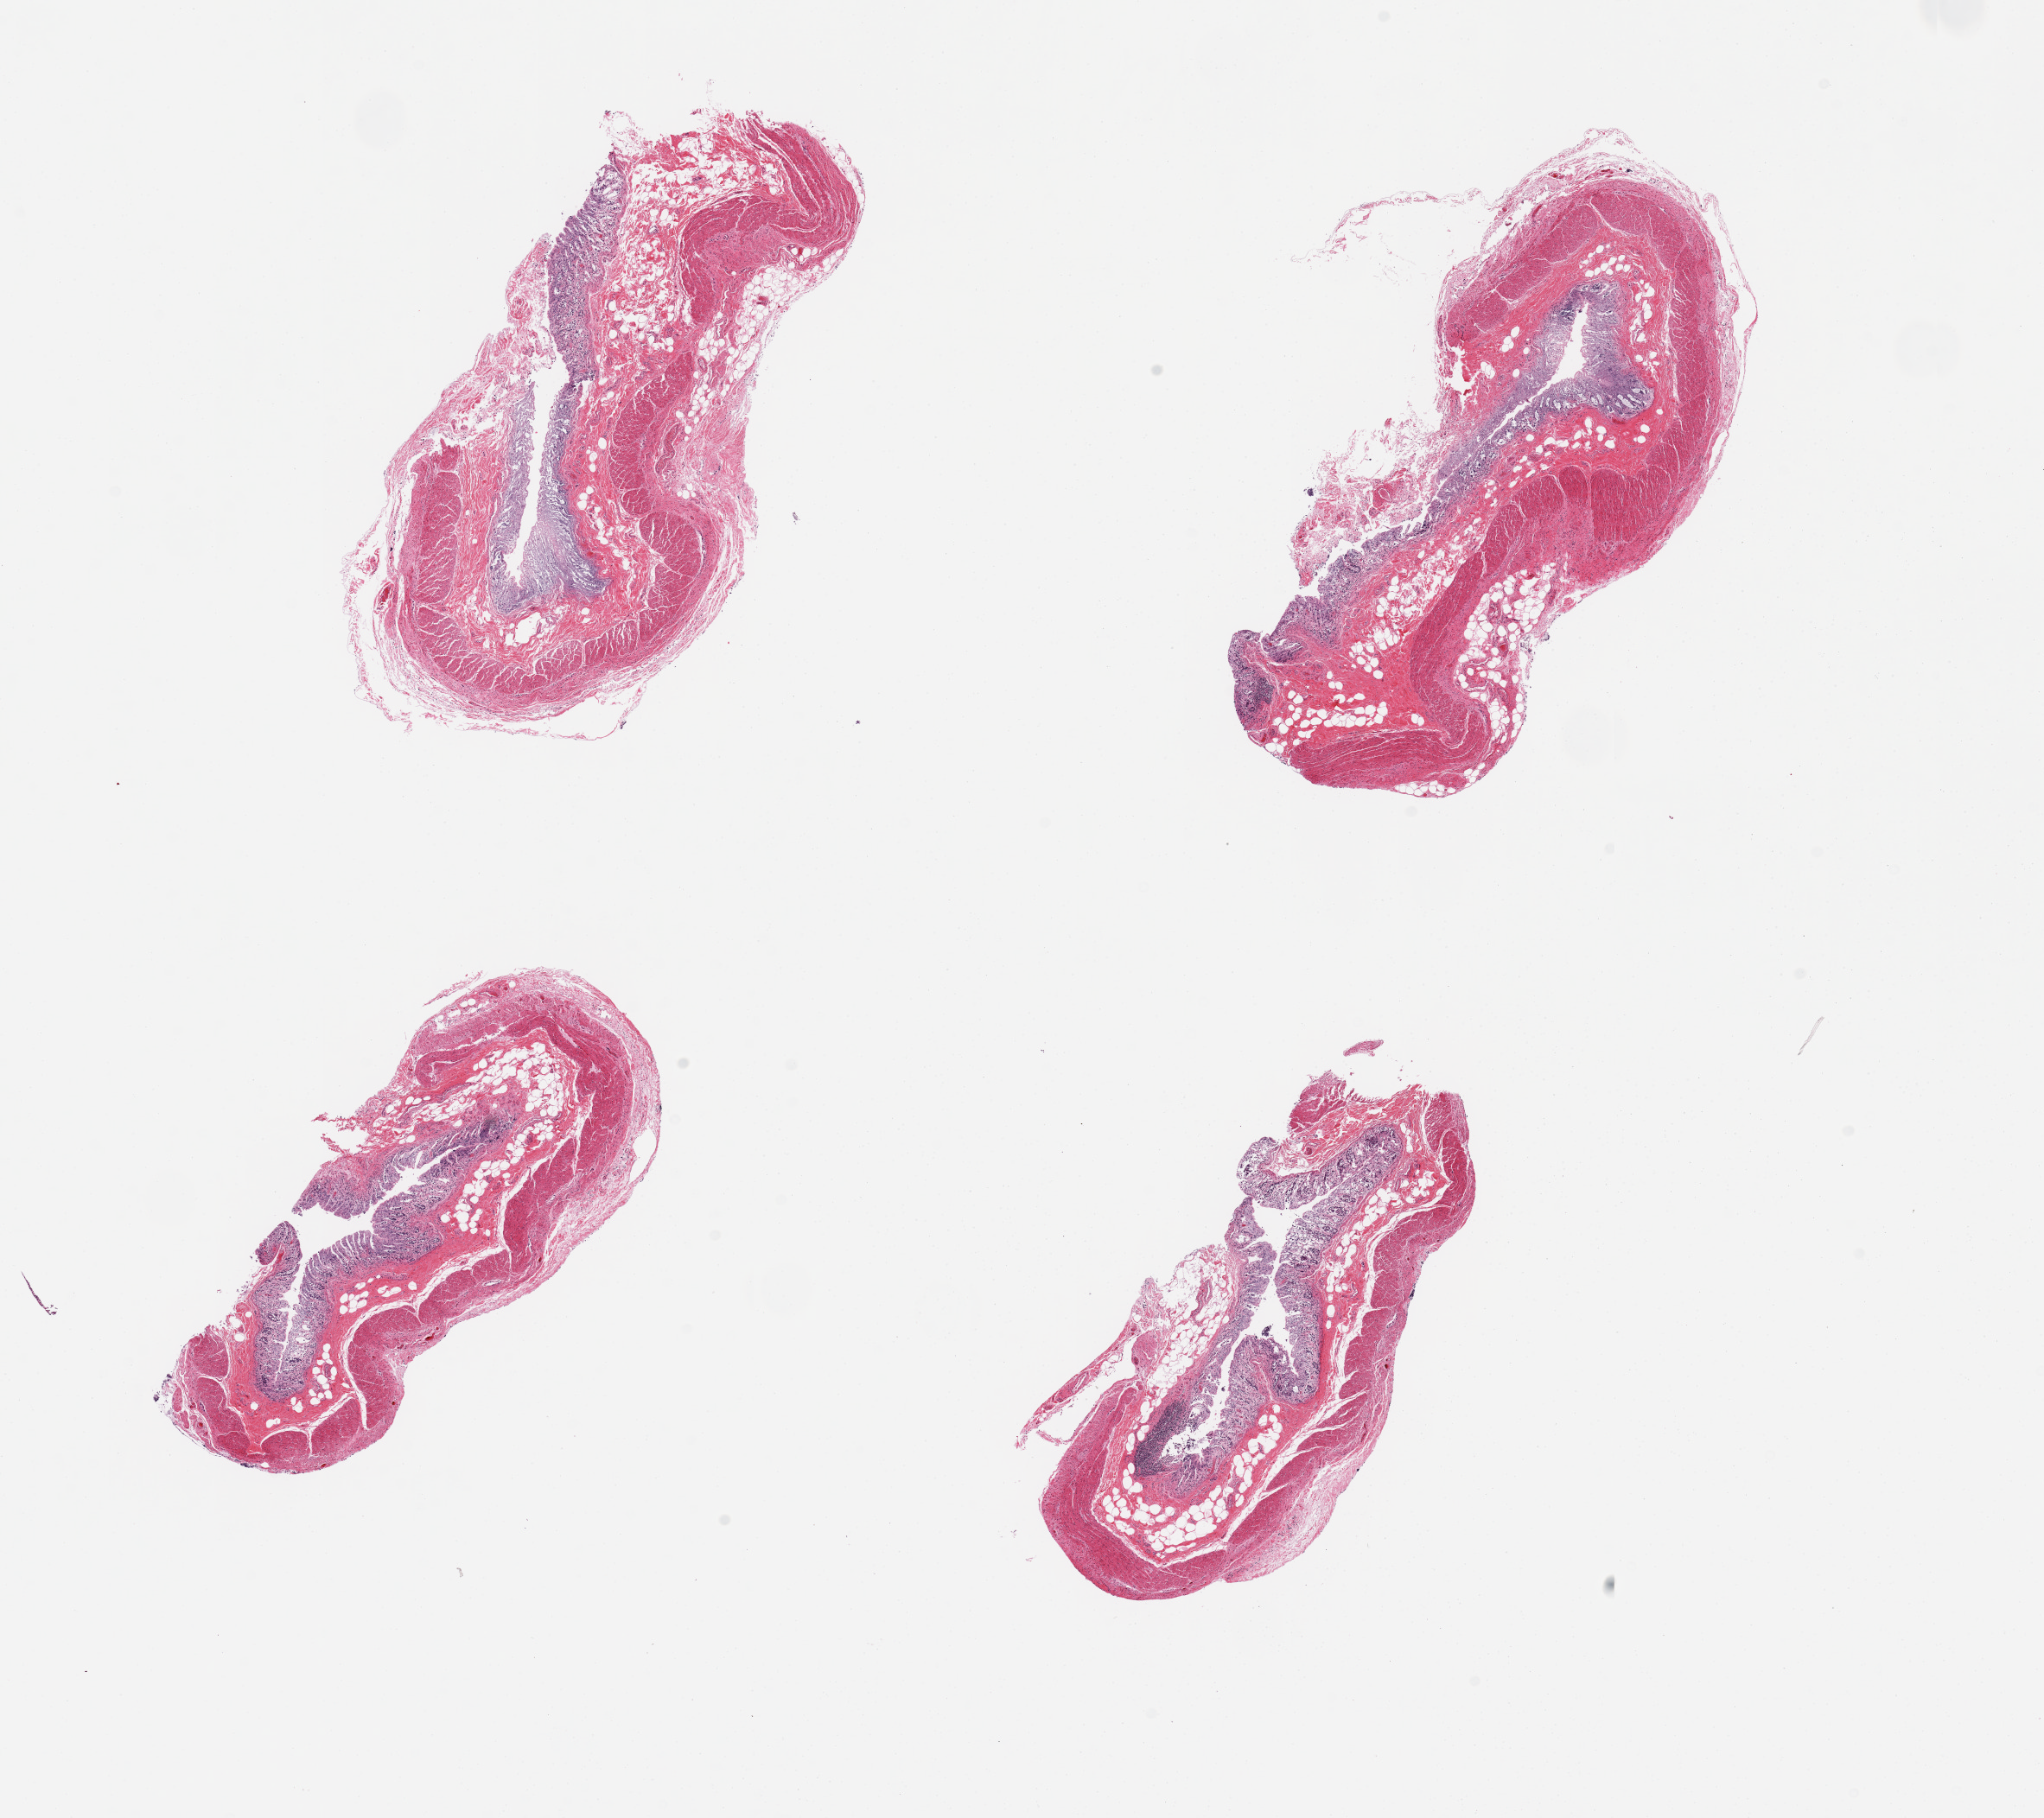
Digitized H&E-stained section — shown as a low-resolution overview of the whole scanned area (about 18.7 x 16.6 mm). PAXgene-fixed, paraffin-embedded tissue. Target tissue: transverse colon. Tissue donor sample. Donor: male.
• review note (as recorded): 4 pieces, mucosa (severely autolyzed) and muscularis